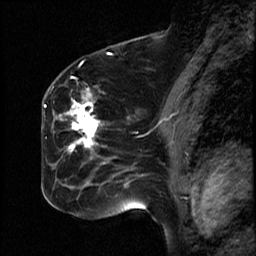
Breast MRI (dynamic contrast-enhanced), one sagittal slice. Position 30 of 50 along the scan axis. Dynamic contrast-enhanced study with each time point stored as its own series, time point 2 of 4 at this slice position (early post-contrast, ordered by acquisition time). 1.5 T. TE 4.2 ms, TR 18.5 ms. 256 × 256 image matrix, field of view 200 × 200 mm. Patient: female, 44 years. Case-level facts recorded for this patient, not image findings: setting: breast cancer imaged before/during neoadjuvant chemotherapy; receptor status: HR-positive, HER2-negative.
Outlined on this slice (semi-automatically segmented with operator editing):
- analysis volume of interest (the breast-tissue region the enhancement analysis was run in; not a lesion): box from (x=59, y=82) to (x=114, y=206) px
- tumour enhancement mask (voxels above the 100 % enhancement threshold inside the analysis volume of interest): (x=67, y=100)–(x=99, y=152)